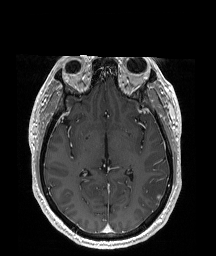
Brain MRI from a brain-tumour surgery series, one axial slice. Slice 104 of 192 in the series (ordered by position). T1-weighted post-contrast. 1 mm slice thickness. 216 × 256 image matrix, field of view 219 × 260 mm. From the clinical record (not read from this slice): histopathology: Glioblastoma; WHO grade: 4; IDH mutation: no; tumour location: Left Temporal Parietal.
Annotated regions visible in this slice (expert manual segmentation):
- tumour: bounding box <142,175,167,204> (left, top, right, bottom; pixels)